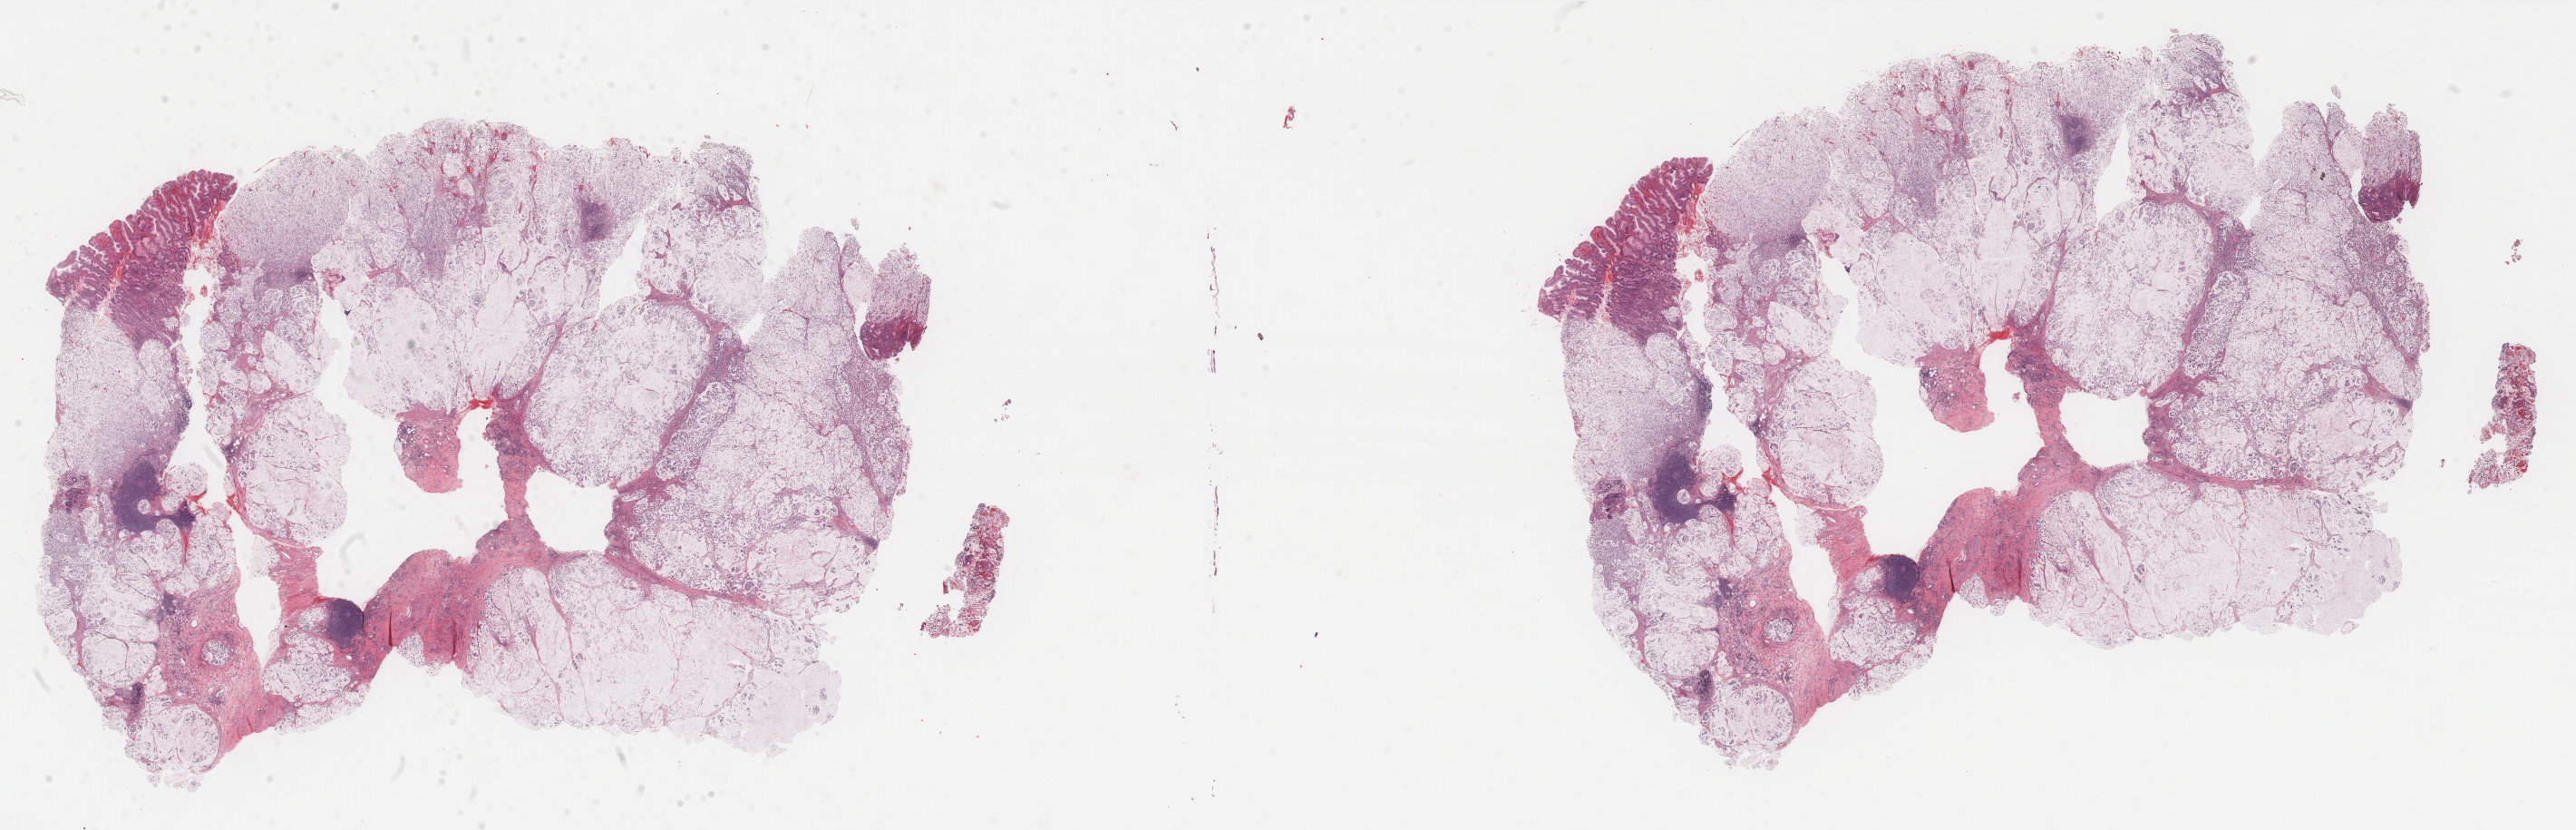
Hematoxylin and eosin (H&E) stained whole-slide image — shown as a low-resolution overview of the whole scanned area (about 44.9 x 14.5 mm, slide scanned at 40x); formalin-fixed paraffin-embedded (FFPE) diagnostic section; stomach, primary tumour sample. Male, age 70 years at initial diagnosis. Histologic grade: G3 (poorly differentiated).
AJCC pathologic stage: IIIB (7th edition). Histologic diagnosis: Mucinous adenocarcinoma (gastric antrum).